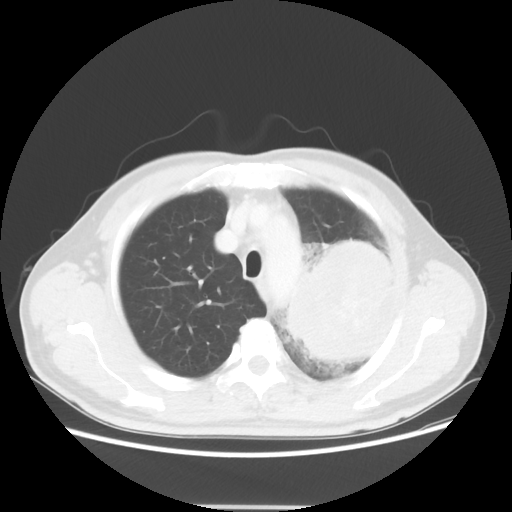
Chest CT, one axial slice. Slice 43 of 53 in the series (ordered by position). Reconstruction kernel STANDARD. 100 kVp. Lung window (W 1500 / L -600 HU). 5 mm slice thickness. 512 × 512 image matrix, field of view 391 × 391 mm. Male patient, age 60 years. Case-level facts recorded for this patient, not image findings: clinical TNM (as recorded): T4 N1 M1a.
Structures marked on this image (rectangle marked by the reading radiologist):
- lung tumour (recorded histology: large cell carcinoma): bounding box [x1, y1, x2, y2] px = [280, 234, 398, 386]